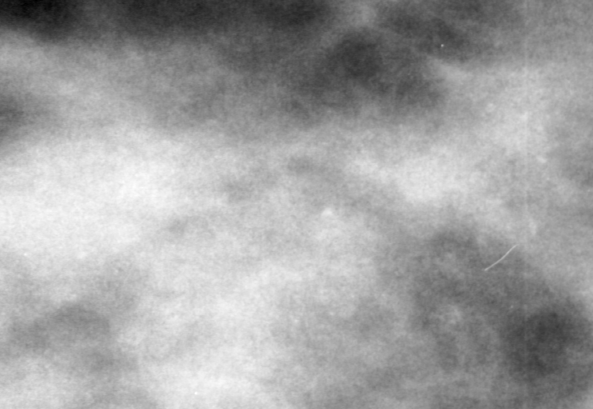
Crop from a digitized film mammogram around one marked abnormality; left breast; MLO view; BI-RADS breast density category 4 (scale 1–4).
- Finding: calcifications, morphology pleomorphic, distribution clustered; BI-RADS assessment category 4; pathology (as recorded): malignant.